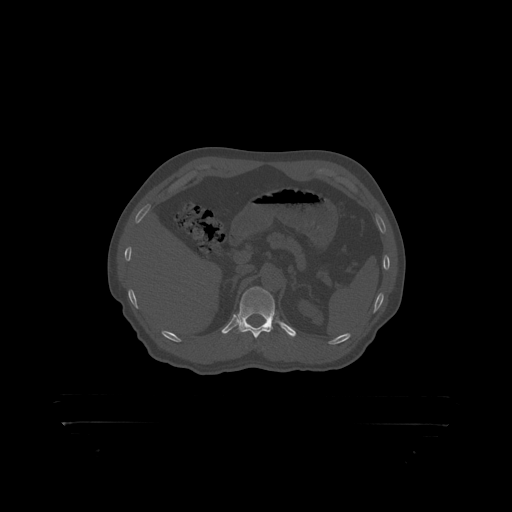
CT including the spine, one axial slice. Position 352 of 399 along the scan axis. 120 kVp. Bone window (W 1800 / L 400 HU). 1.25 mm slice thickness. 512 × 512 image matrix, field of view 650 × 650 mm. Male patient, age 46 years. From the clinical record (not read from this slice): primary cancer: skin.
Outlined on this slice (semi-automatically segmented with operator editing):
- T12 vertebra: bounding box <239,287,276,319> (left, top, right, bottom; pixels)